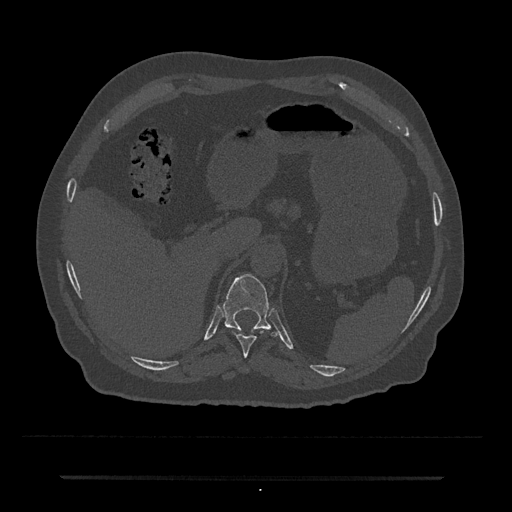
CT including the spine, one axial slice. Slice 200 of 797 in the series (ordered by position). Reconstruction kernel Br40s/3. Bone window (W 1800 / L 400 HU). 0.5 mm slice thickness. 512 × 512 image matrix. Male patient, age 69 years. From the clinical record (not read from this slice): primary cancer: prostate.
Outlined on this slice (semi-automatic segmentation, software-assisted and operator-edited):
- T10 vertebra: bounding box (x1, y1, x2, y2) in pixels: (232, 331, 264, 357)
- T11 vertebra: (223, 273, 280, 338)